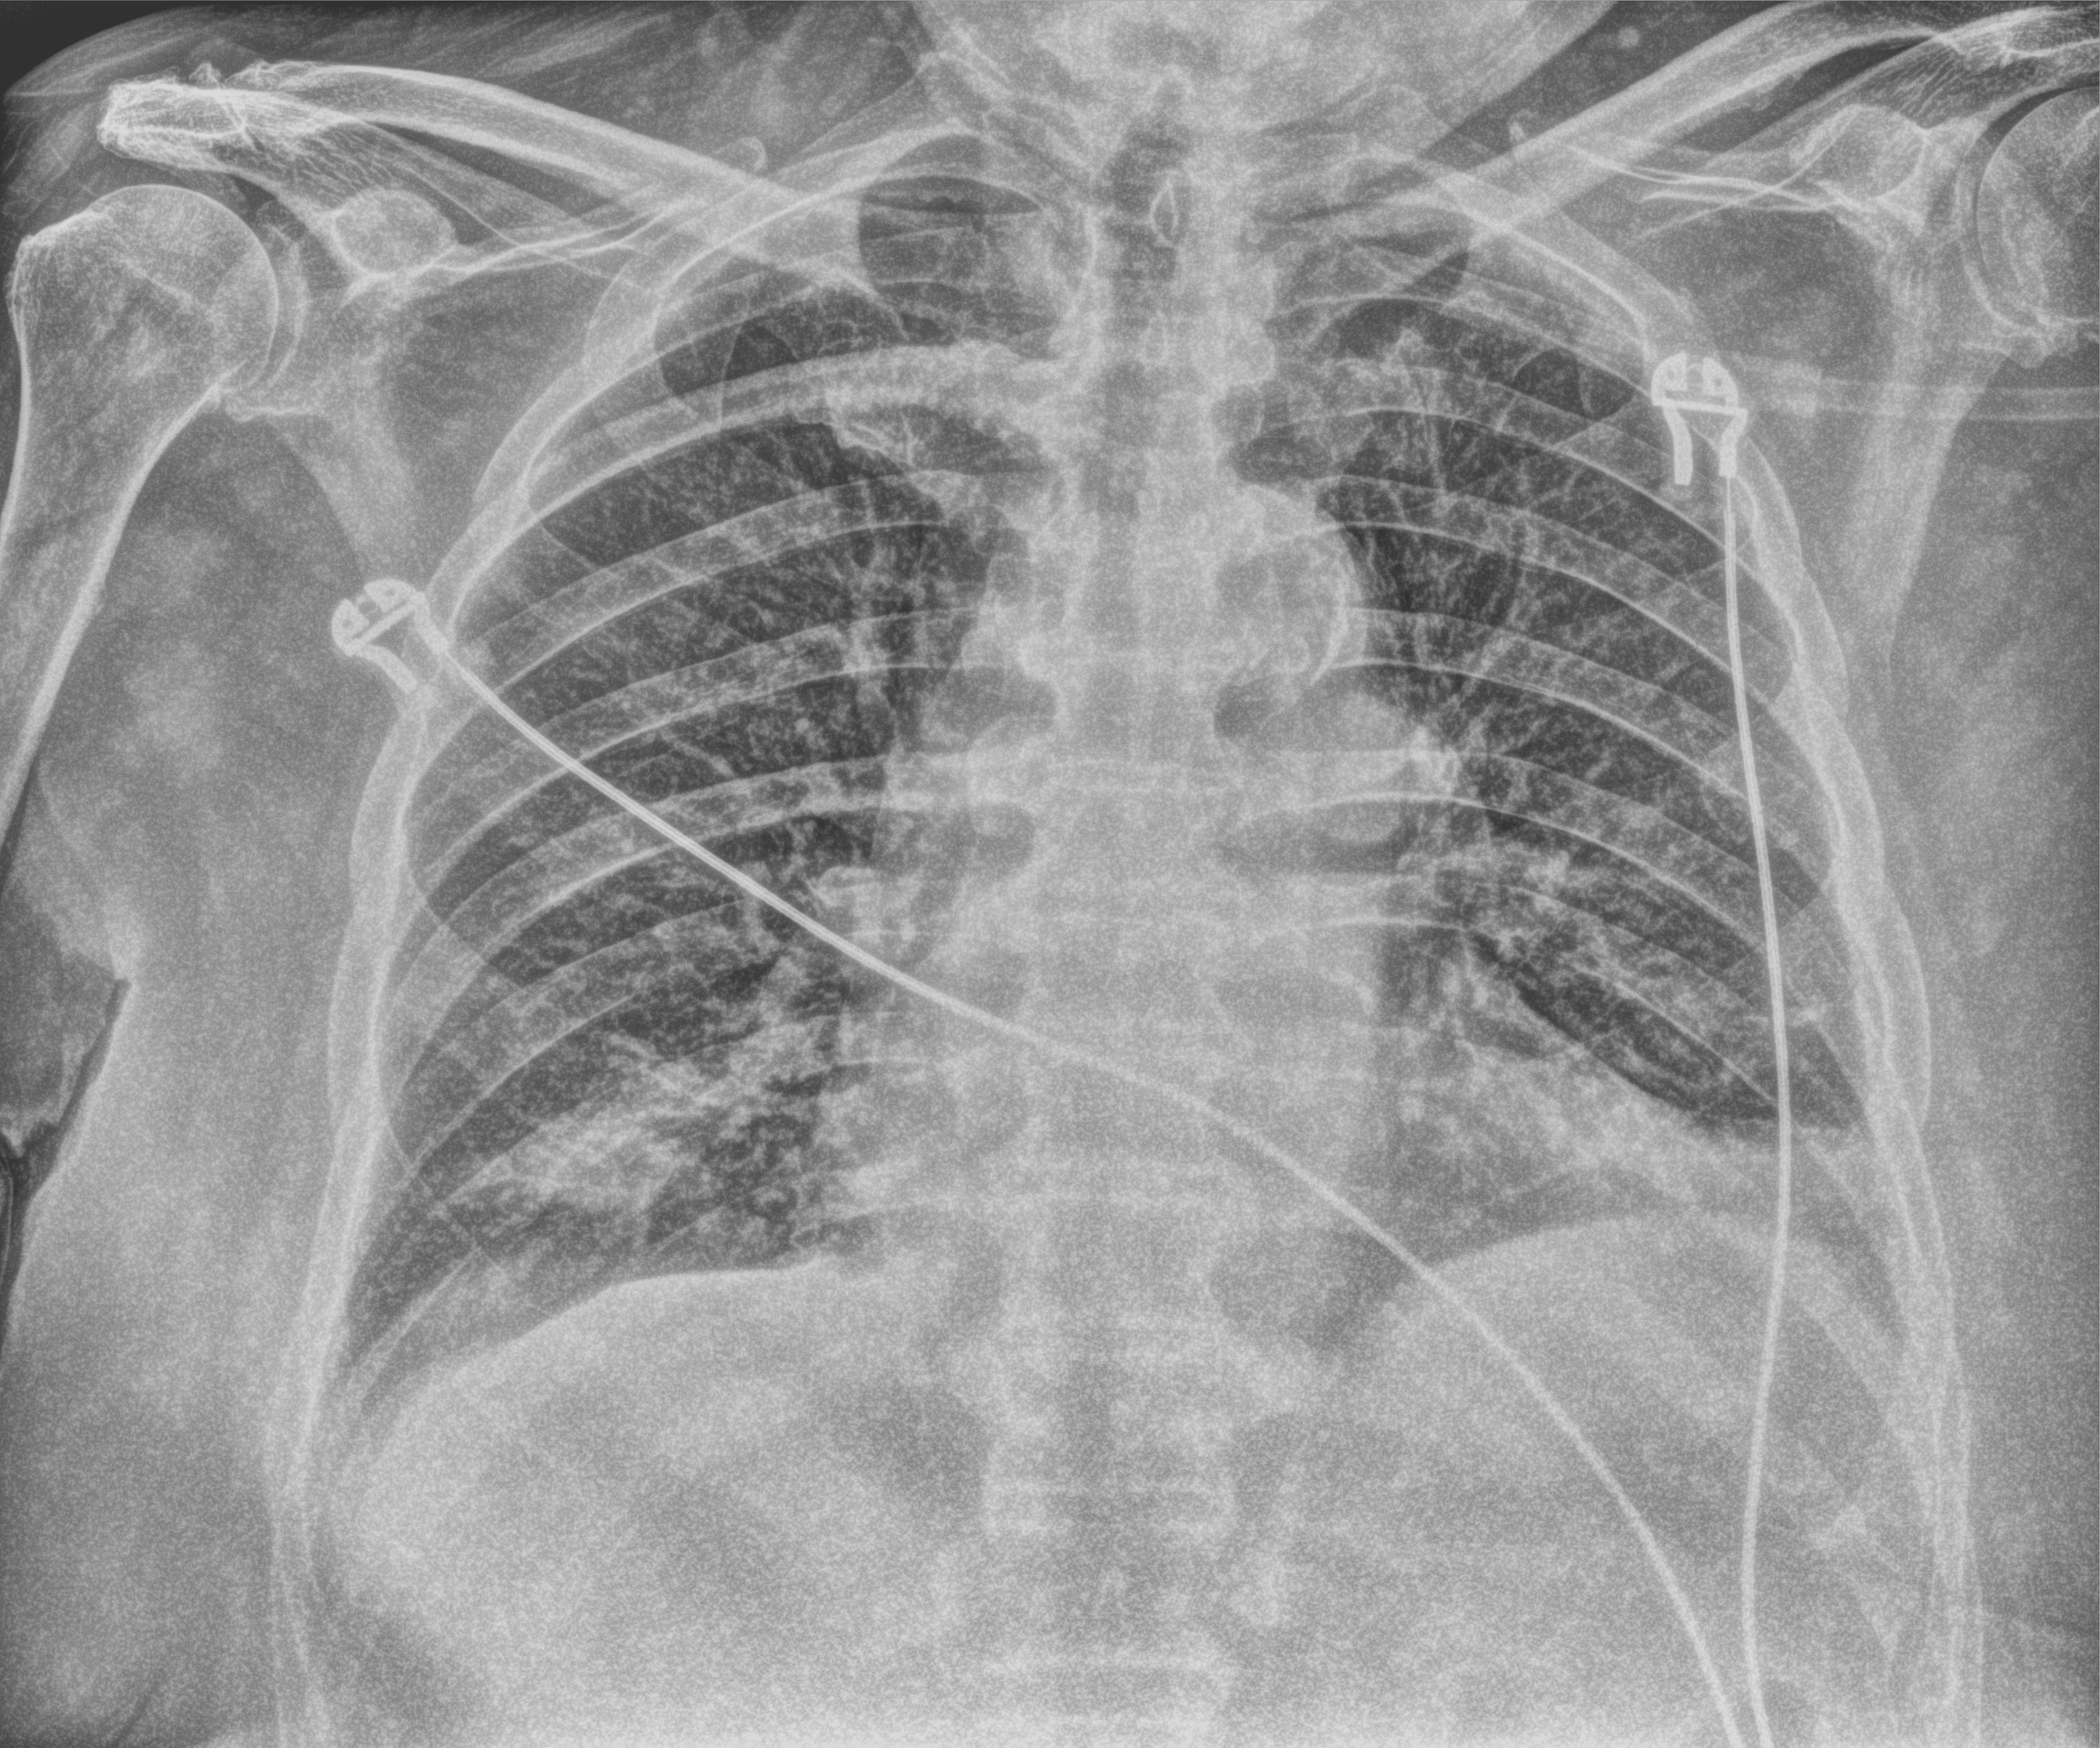
Chest X-ray (portable). Patient hospitalised with COVID-19; male, aged 75–90 years.
From the hospital-stay record, not from the radiograph (when in the stay this image was taken is not recorded): admitted to intensive care during this hospital stay: no; diabetes (admission record): yes; chronic kidney disease (admission record): yes.